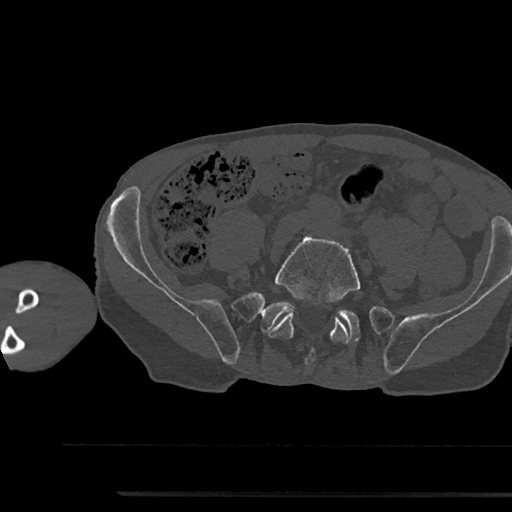
CT including the spine, one axial slice; bone window (W 1800 / L 400 HU); 0.5 mm slice thickness; 512 × 512 image matrix, field of view 367 × 367 mm. Patient: male, 79 years. From the clinical record (not read from this slice): primary cancer: prostate.
Structures marked on this image (semi-automatically segmented with operator editing):
- L5 vertebra: bounding box <268,236,361,364> (left, top, right, bottom; pixels)